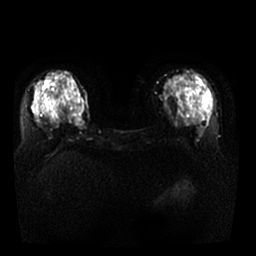
Breast MRI, one axial slice. Position 14 of 29 along the scan axis. Diffusion-weighted series; image 2 of 4 stored at this slice position (different b-values; order by instance number). 1.5 T. 4 mm slice thickness. 256 × 256 image matrix, field of view 340 × 340 mm. Female patient.
Structures marked on this image (outlined manually by an expert reader):
- tumour on diffusion-weighted imaging: bounding box <75,119,84,130> (left, top, right, bottom; pixels)